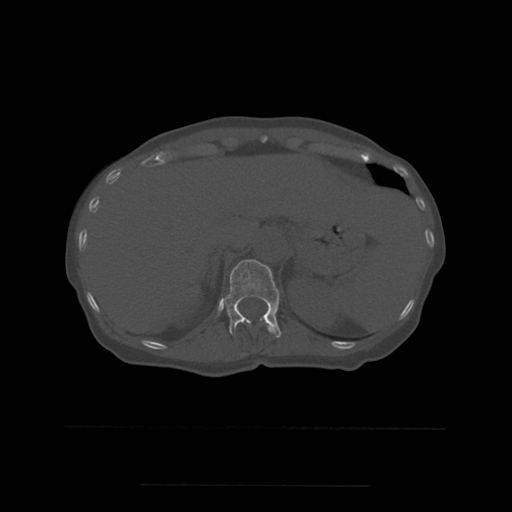
CT including the spine, one axial slice. Position 264 of 544 along the scan axis. Bone window (W 1800 / L 400 HU). 512 × 512 image matrix. Patient age 58 years. Case-level facts recorded for this patient, not image findings: primary cancer: lung.
Outlined on this slice (semi-automatic segmentation, software-assisted and operator-edited):
- T11 vertebra: bounding box [x1, y1, x2, y2] px = [239, 320, 274, 333]
- T12 vertebra: [223, 260, 282, 338]